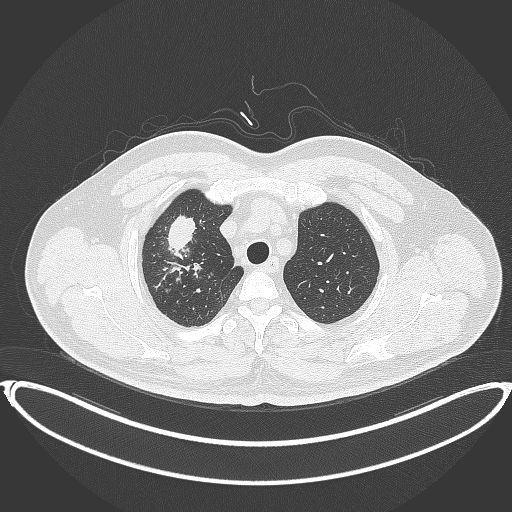
Chest CT, one axial slice; position 320 of 399 along the scan axis; 120 kVp; lung window (W 1500 / L -600 HU); 1 mm slice thickness; 512 × 512 image matrix. Male patient, age 53 years. Case-level facts recorded for this patient, not image findings: clinical TNM (as recorded): T2a N0 M0.
Annotated regions visible in this slice (bounding box drawn by a radiologist):
- lung tumour (recorded histology: adenocarcinoma): bounding box <164,212,201,260> (left, top, right, bottom; pixels)